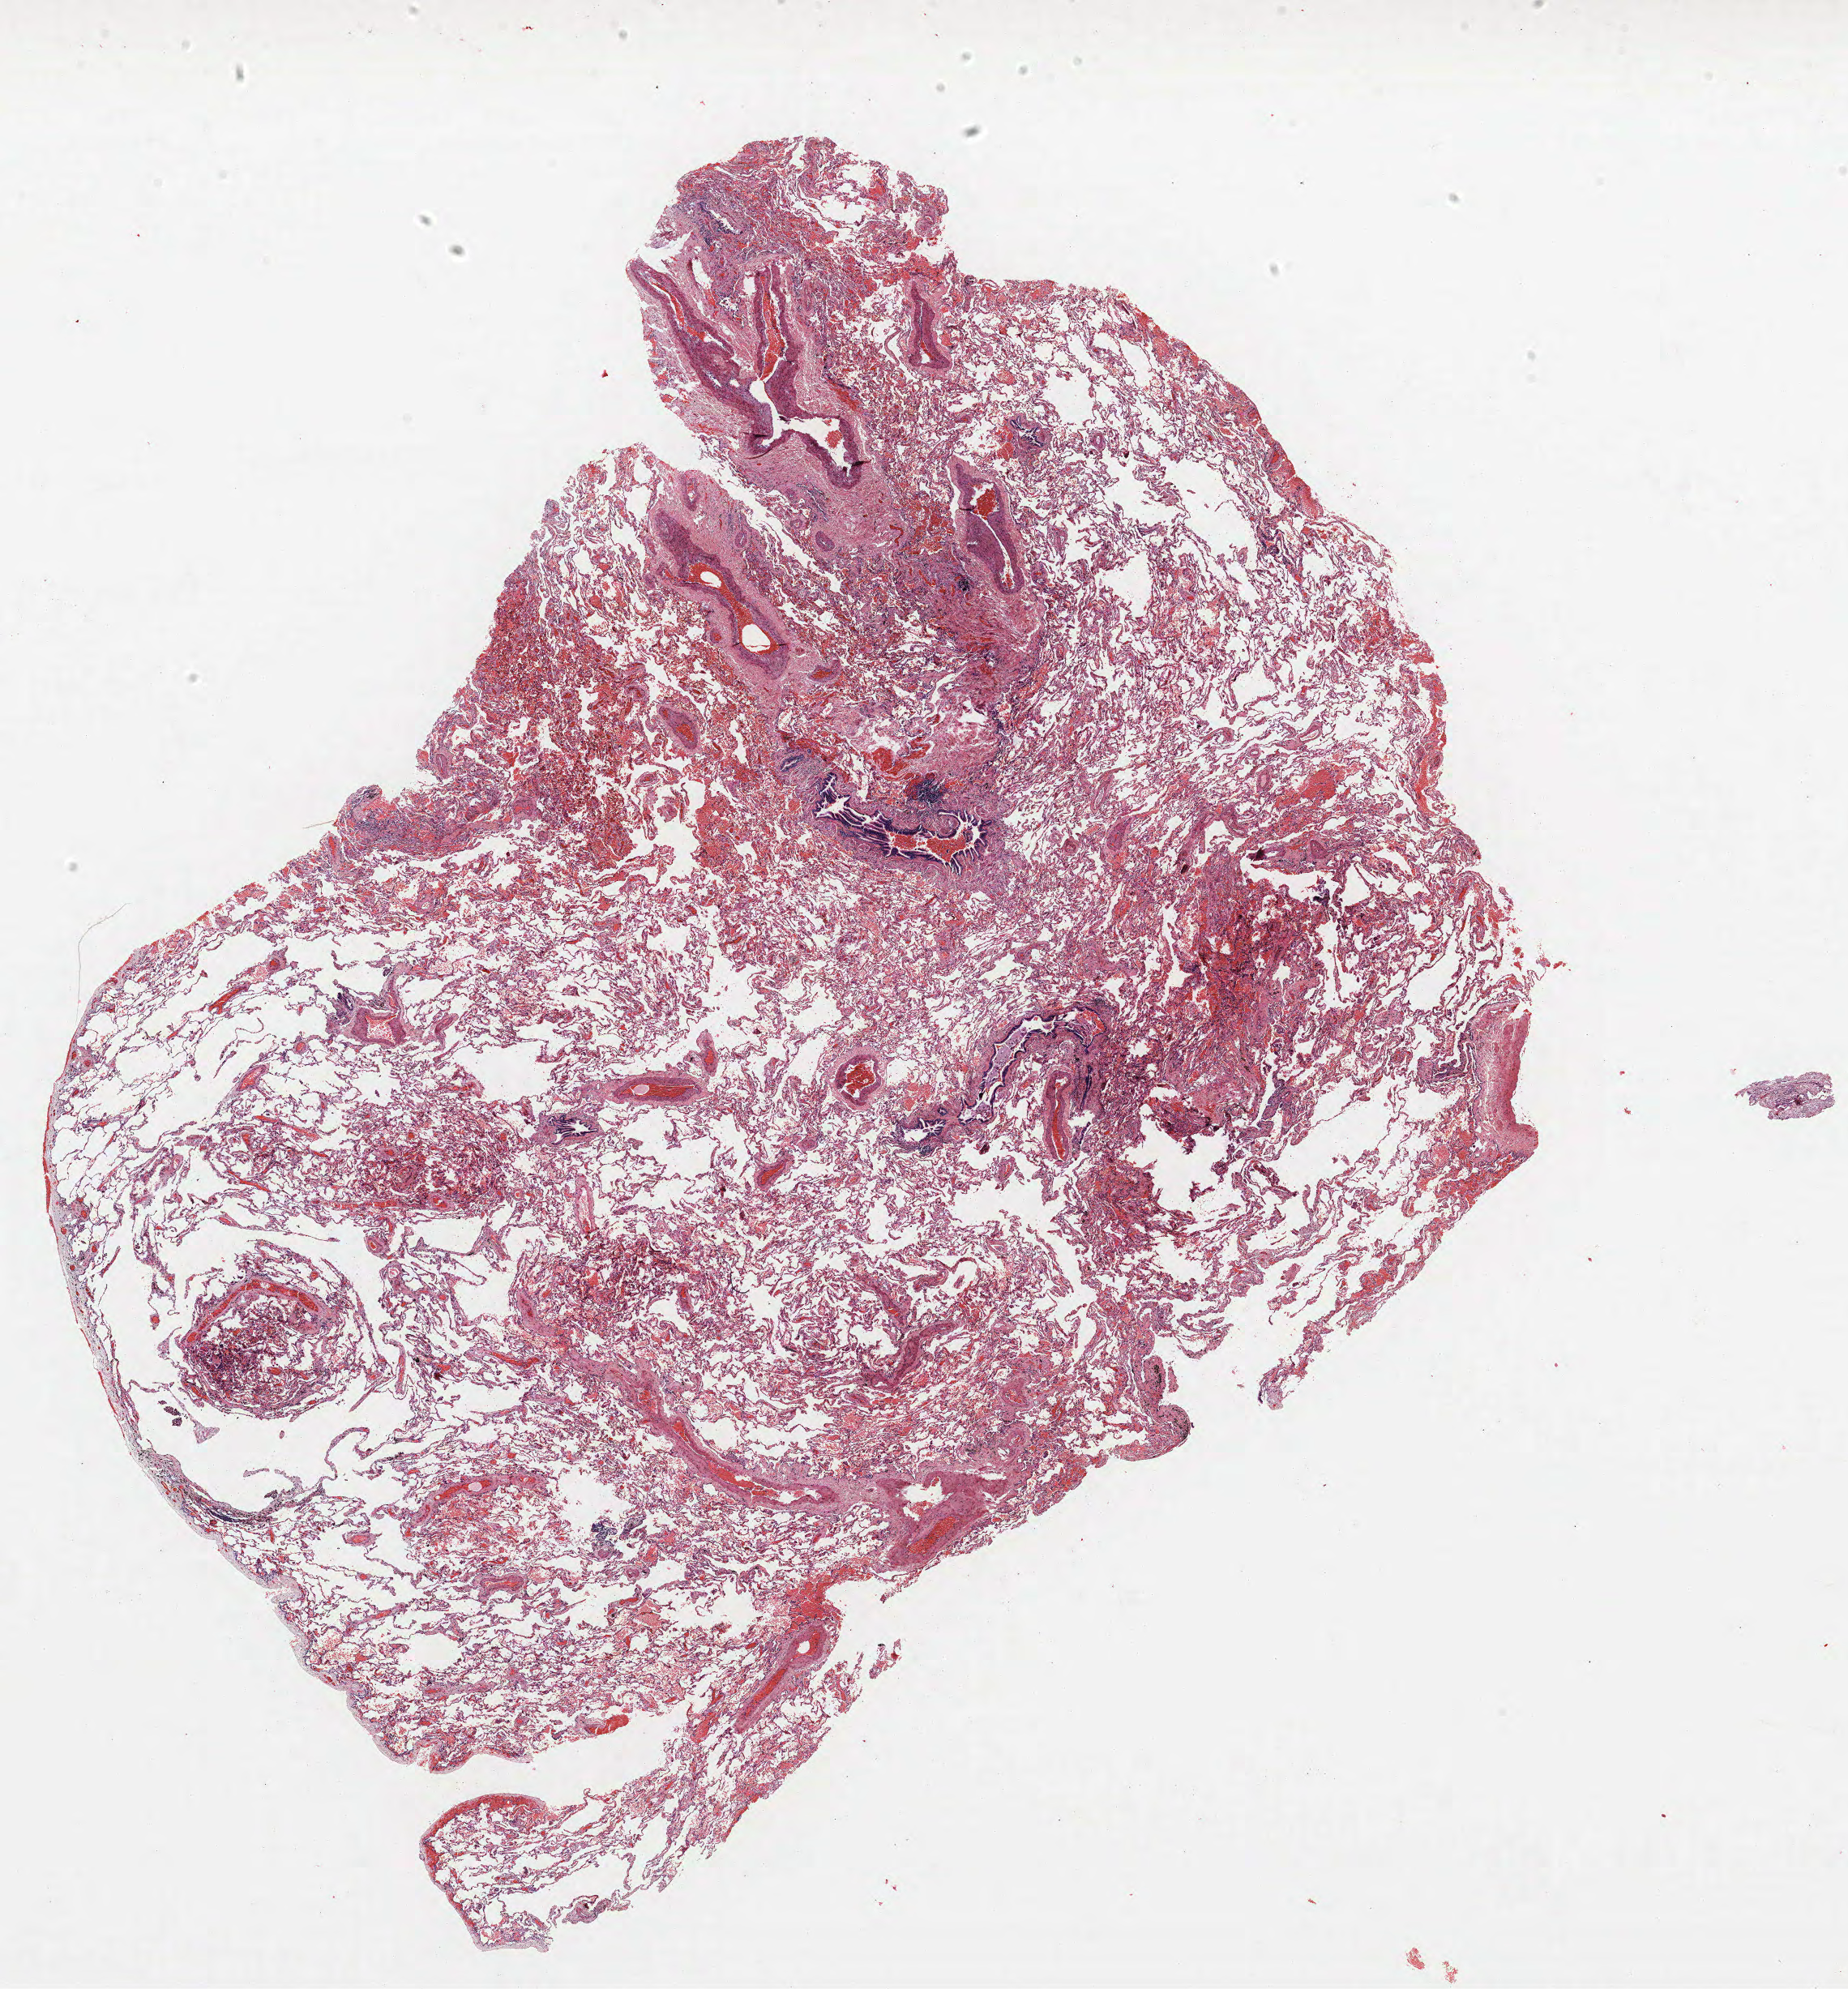
Whole-slide histology image, H&E — whole scanned area (about 18.2 x 19.6 mm) shown as a low-resolution overview. FFPE section. Lung tissue. Male, age 59 at enrolment. Grade: undifferentiated (G4).
* stage (AJCC 6th edition): IA
* tumour size (pathology): 25 mm
* primary tumour location (clinical record): right upper lobe
* participant's lung-cancer diagnosis: Large cell carcinoma, NOS (ICD-O-3 8012/3)